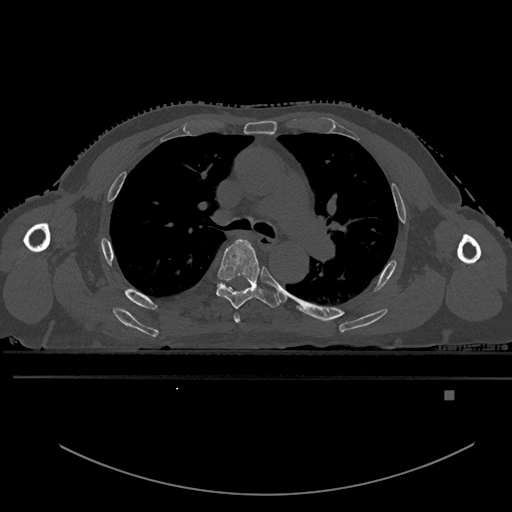
CT including the spine, one axial slice; bone window (W 1800 / L 400 HU); 0.5 mm slice thickness; 512 × 512 image matrix, field of view 456 × 456 mm. Male patient, age 82 years. From the clinical record (not read from this slice): primary cancer: prostate.
Outlined on this slice (semi-automatically segmented with operator editing):
- T4 vertebra: bounding box (x1, y1, x2, y2) in pixels: (234, 313, 241, 324)
- T5 vertebra: (216, 239, 279, 310)